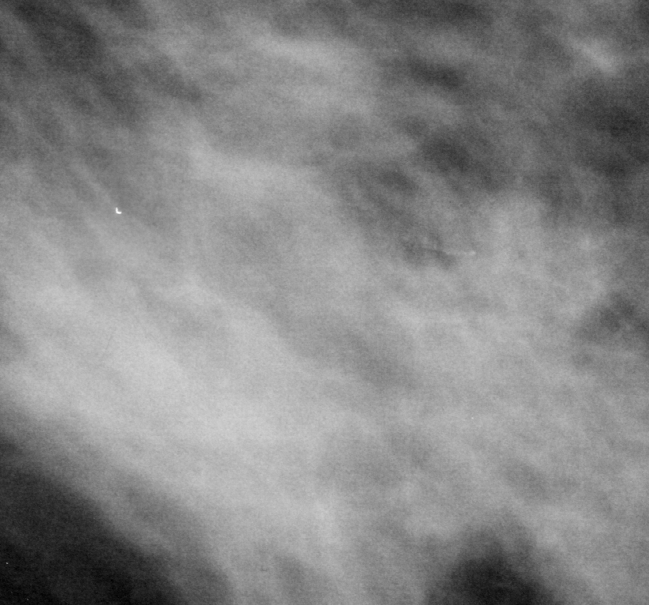
Crop from a digitized film mammogram around one marked abnormality, left breast, MLO view, BI-RADS breast density category 2 (scale 1–4).
- Finding: mass, shape irregular, margins ill defined; BI-RADS assessment category 5; pathology result (as recorded, not read from the image): malignant.